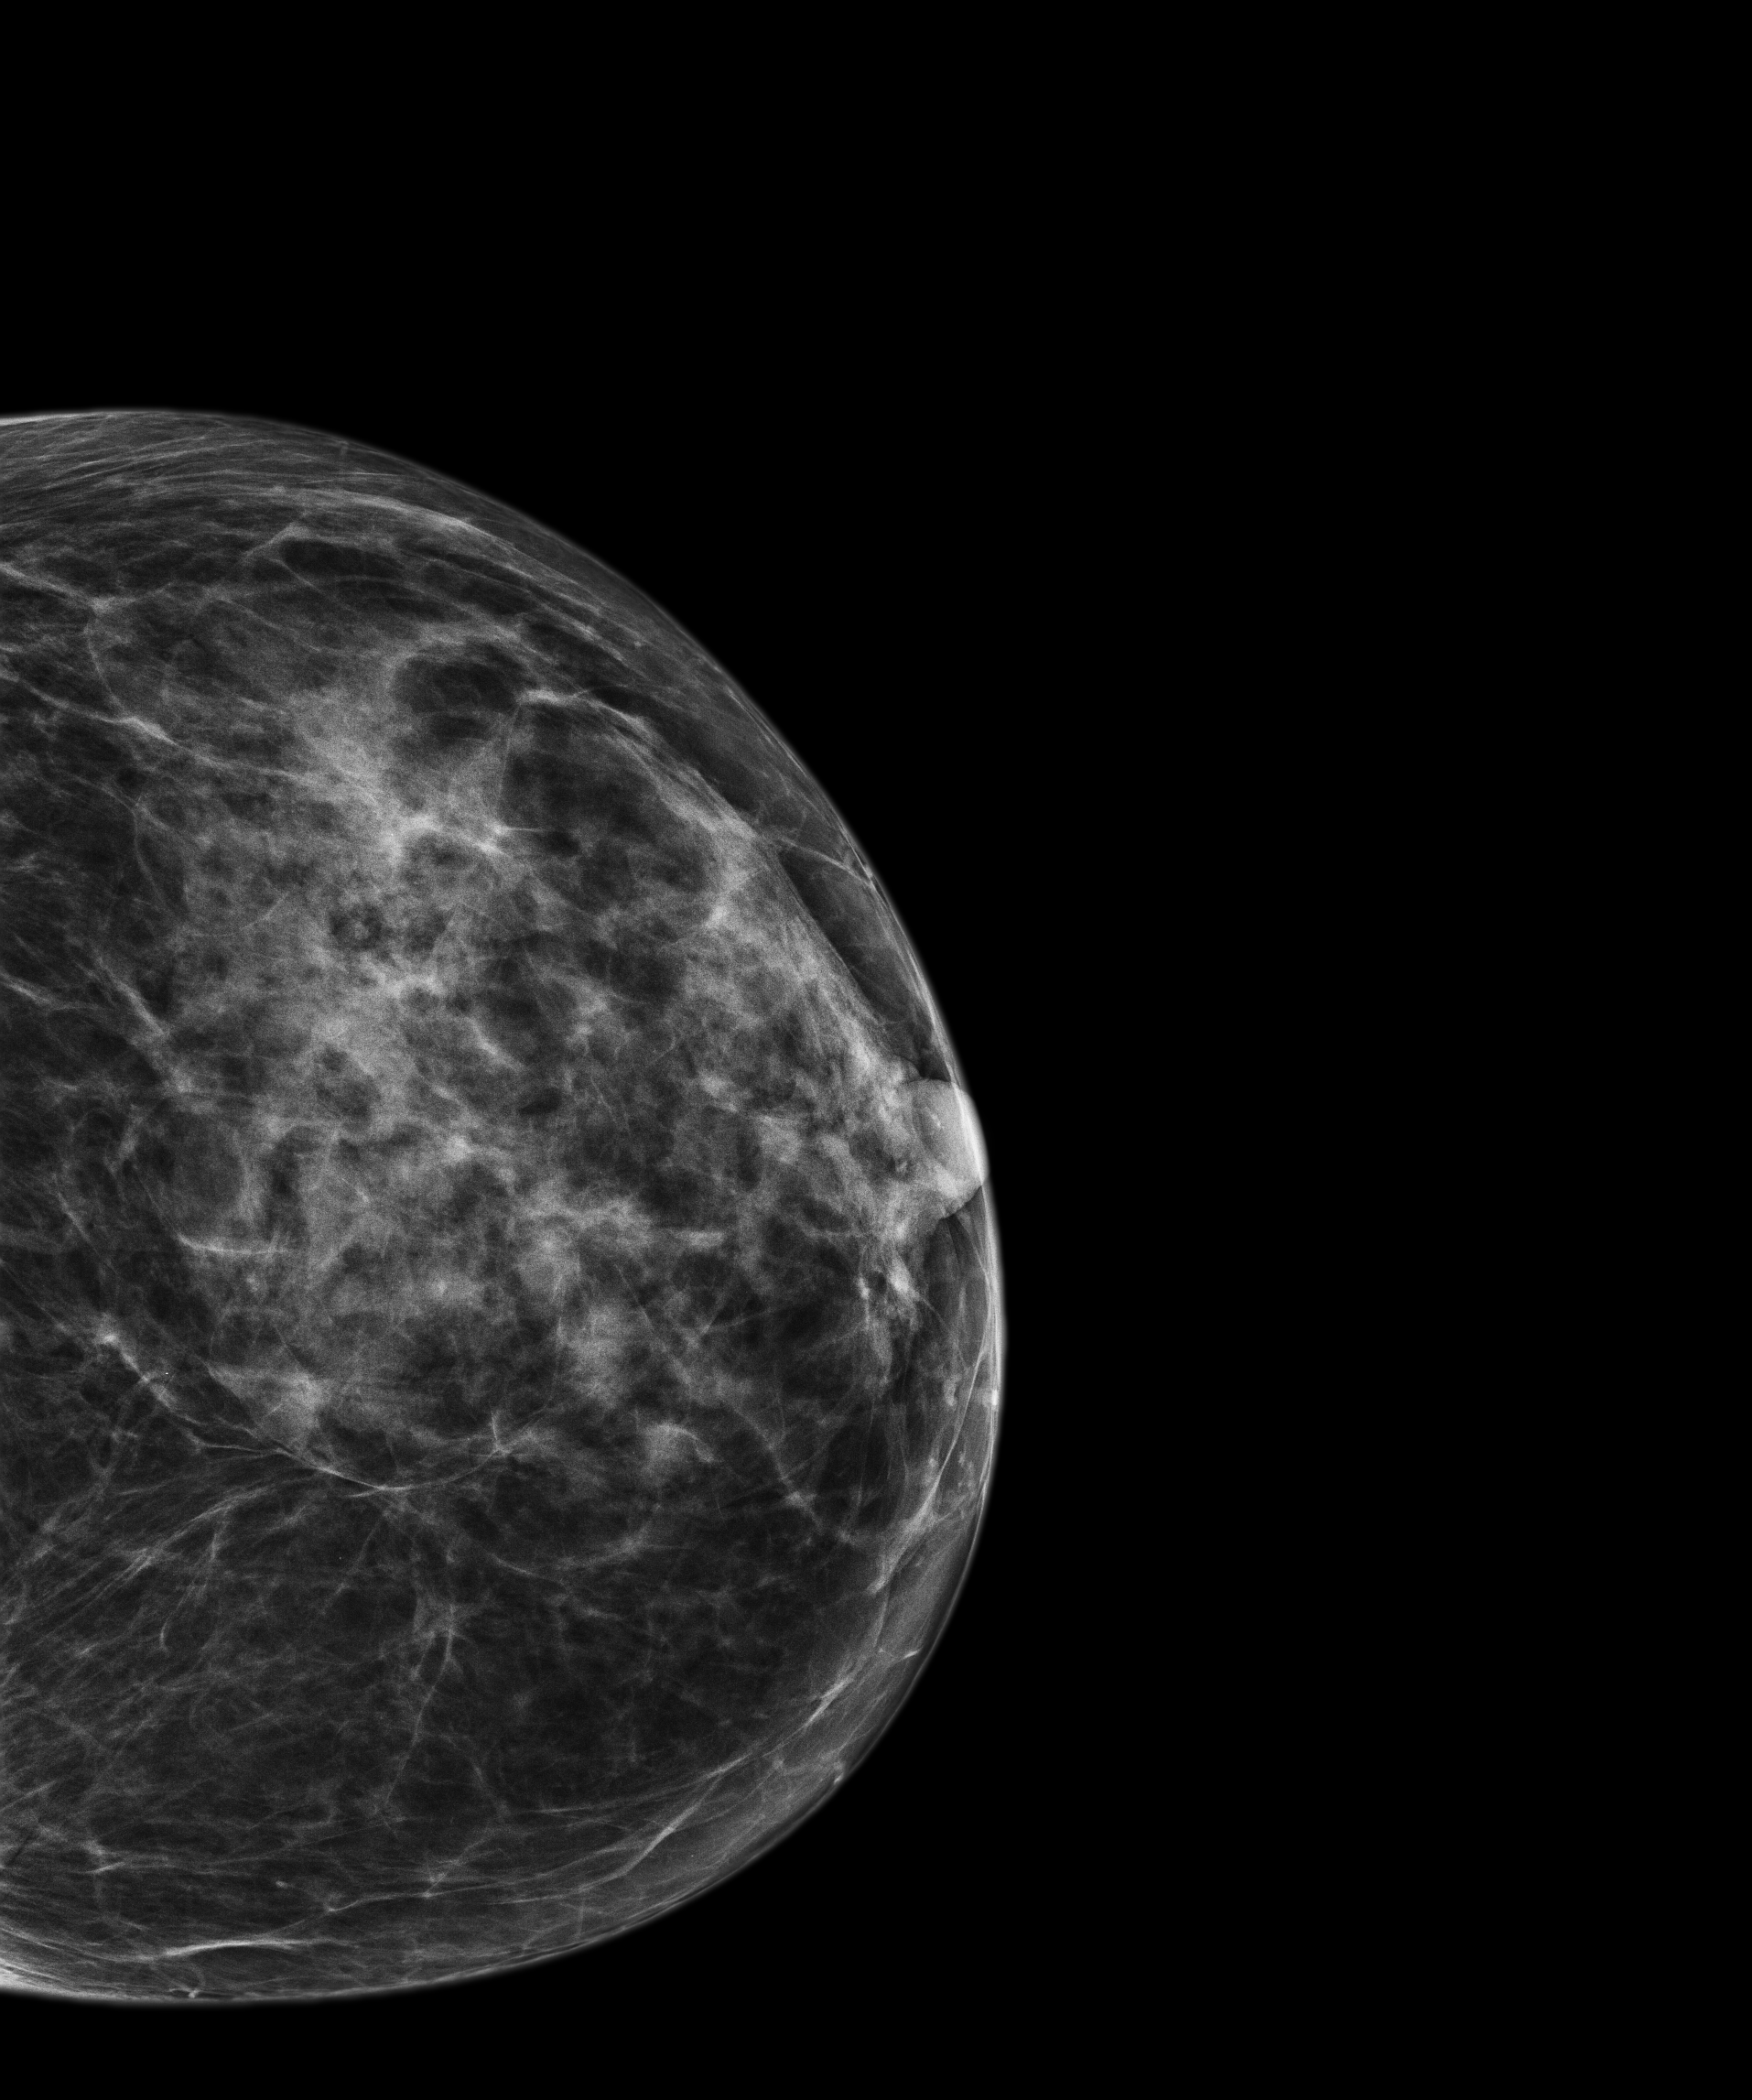
Annual screening mammography examination, system: Senographe Pristina.
Image type: full-field digital mammogram. Breast: left. Projection: cranio-caudal projection.